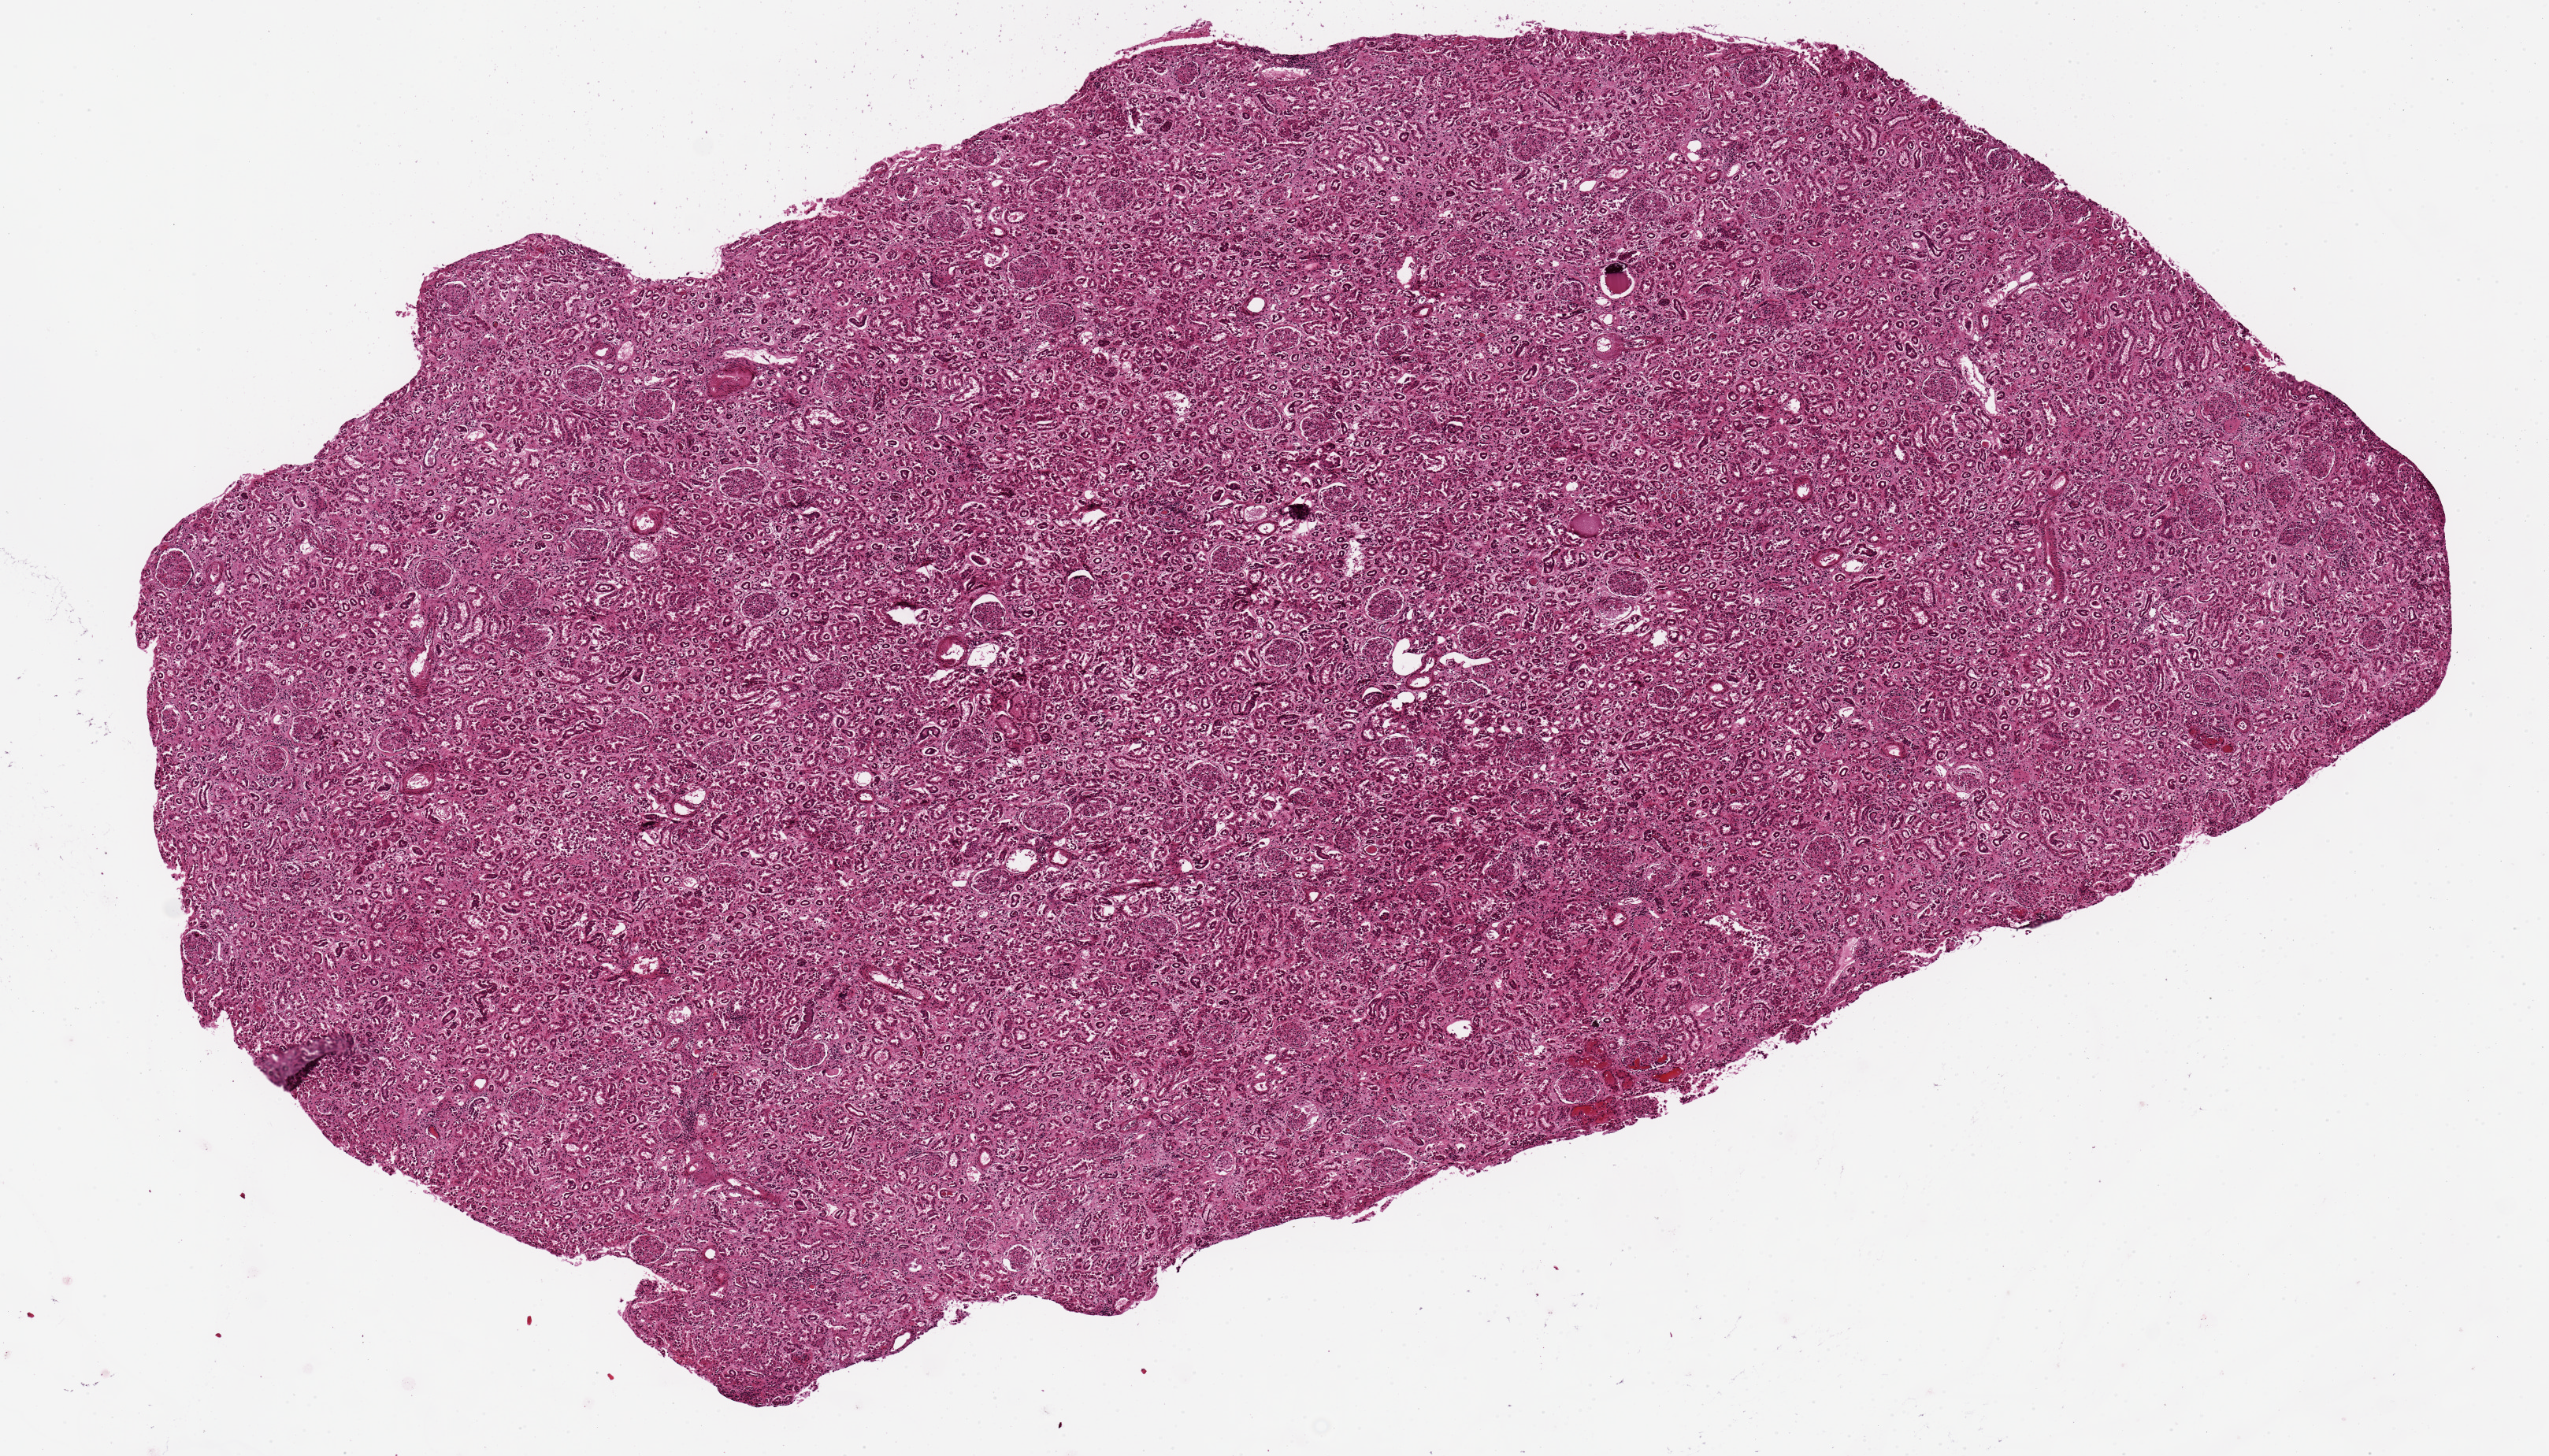
Whole-slide image, hematoxylin and eosin (H&E) stain — whole scanned area (about 12.8 x 7.3 mm) shown as a low-resolution overview, PAXgene-fixed, paraffin-embedded tissue, section of renal cortex (target tissue), tissue donor sample. Donor: female.
* pathologist's review note for this sample: Not medulla, all cortex